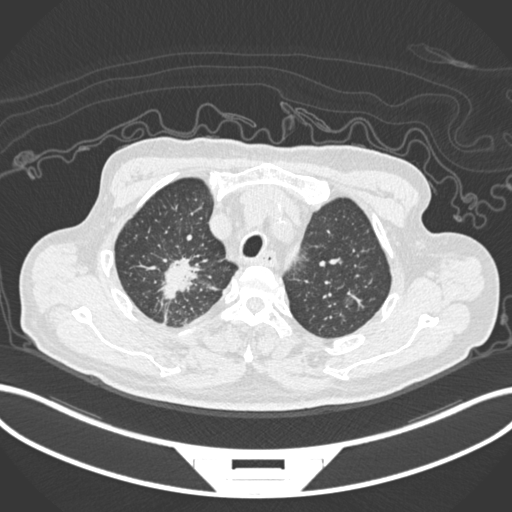
Chest CT, one axial slice. Slice 175 of 207 in the series (ordered by position). Reconstruction kernel B30f. Lung window (W 1500 / L -600 HU). 1 mm slice thickness. 512 × 512 image matrix, field of view 400 × 400 mm. Male patient, age 69 years. Case-level facts recorded for this patient, not image findings: clinical TNM (as recorded): T1c N1 M1.
Annotated regions visible in this slice (bounding box drawn by a radiologist):
- lung tumour (recorded histology: adenocarcinoma): box from (x=158, y=256) to (x=212, y=315) px